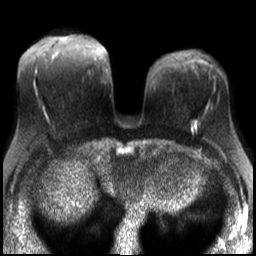
Breast MRI, one axial slice; position 13 of 30 along the scan axis; diffusion-weighted series; image 2 of 4 stored at this slice position (different b-values; order by instance number); 3 T; 4 mm slice thickness; 256 × 256 image matrix, field of view 320 × 320 mm. Female patient.
Structures marked on this image (outlined manually by an expert reader):
- tumour on diffusion-weighted imaging: box from (x=192, y=122) to (x=196, y=128) px